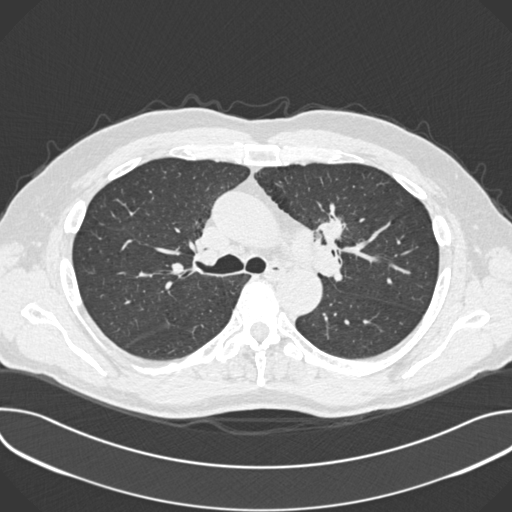
Low-dose screening chest CT, one axial slice; slice 249 of 361 in the series (ordered by position); 120 kVp; lung window (W 1500 / L -600 HU); 1 mm slice thickness; 512 × 512 image matrix, field of view 380 × 380 mm.
Outlined on this slice (expert manual segmentation):
- lesion 1 (tumor, upper lobe of left lung): box from (x=316, y=211) to (x=345, y=248) px